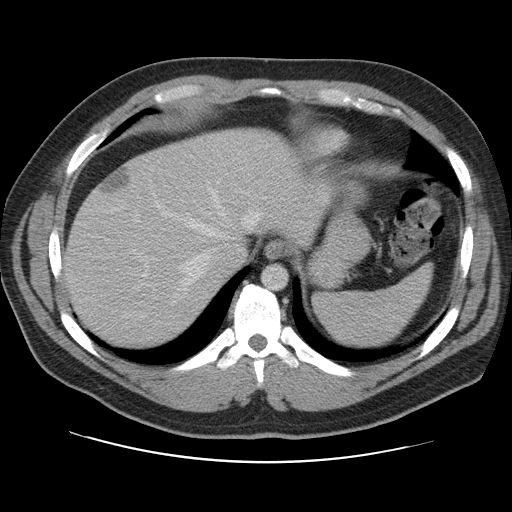
Contrast-enhanced abdominal CT, one axial slice. Slice 90 of 109 in the series (ordered by position). Intravenous contrast given. Soft-tissue window (W 400 / L 40 HU). 5 mm slice thickness. 512 × 512 image matrix, field of view 402 × 402 mm. Male patient, age 35 years. From the clinical record (not read from this slice): diagnosis: colorectal cancer liver metastases, imaged before liver resection; multiple liver metastases: yes; largest metastasis: 2.8 cm; disease in both lobes: yes.
Outlined on this slice (outlined manually by an expert reader):
- hepatic veins: box from (x=139, y=181) to (x=262, y=318) px
- liver: (x=64, y=129)–(x=326, y=350)
- planned liver remnant (the part of the liver to remain after resection): (x=65, y=128)–(x=326, y=349)
- liver metastasis: (x=103, y=169)–(x=131, y=194)